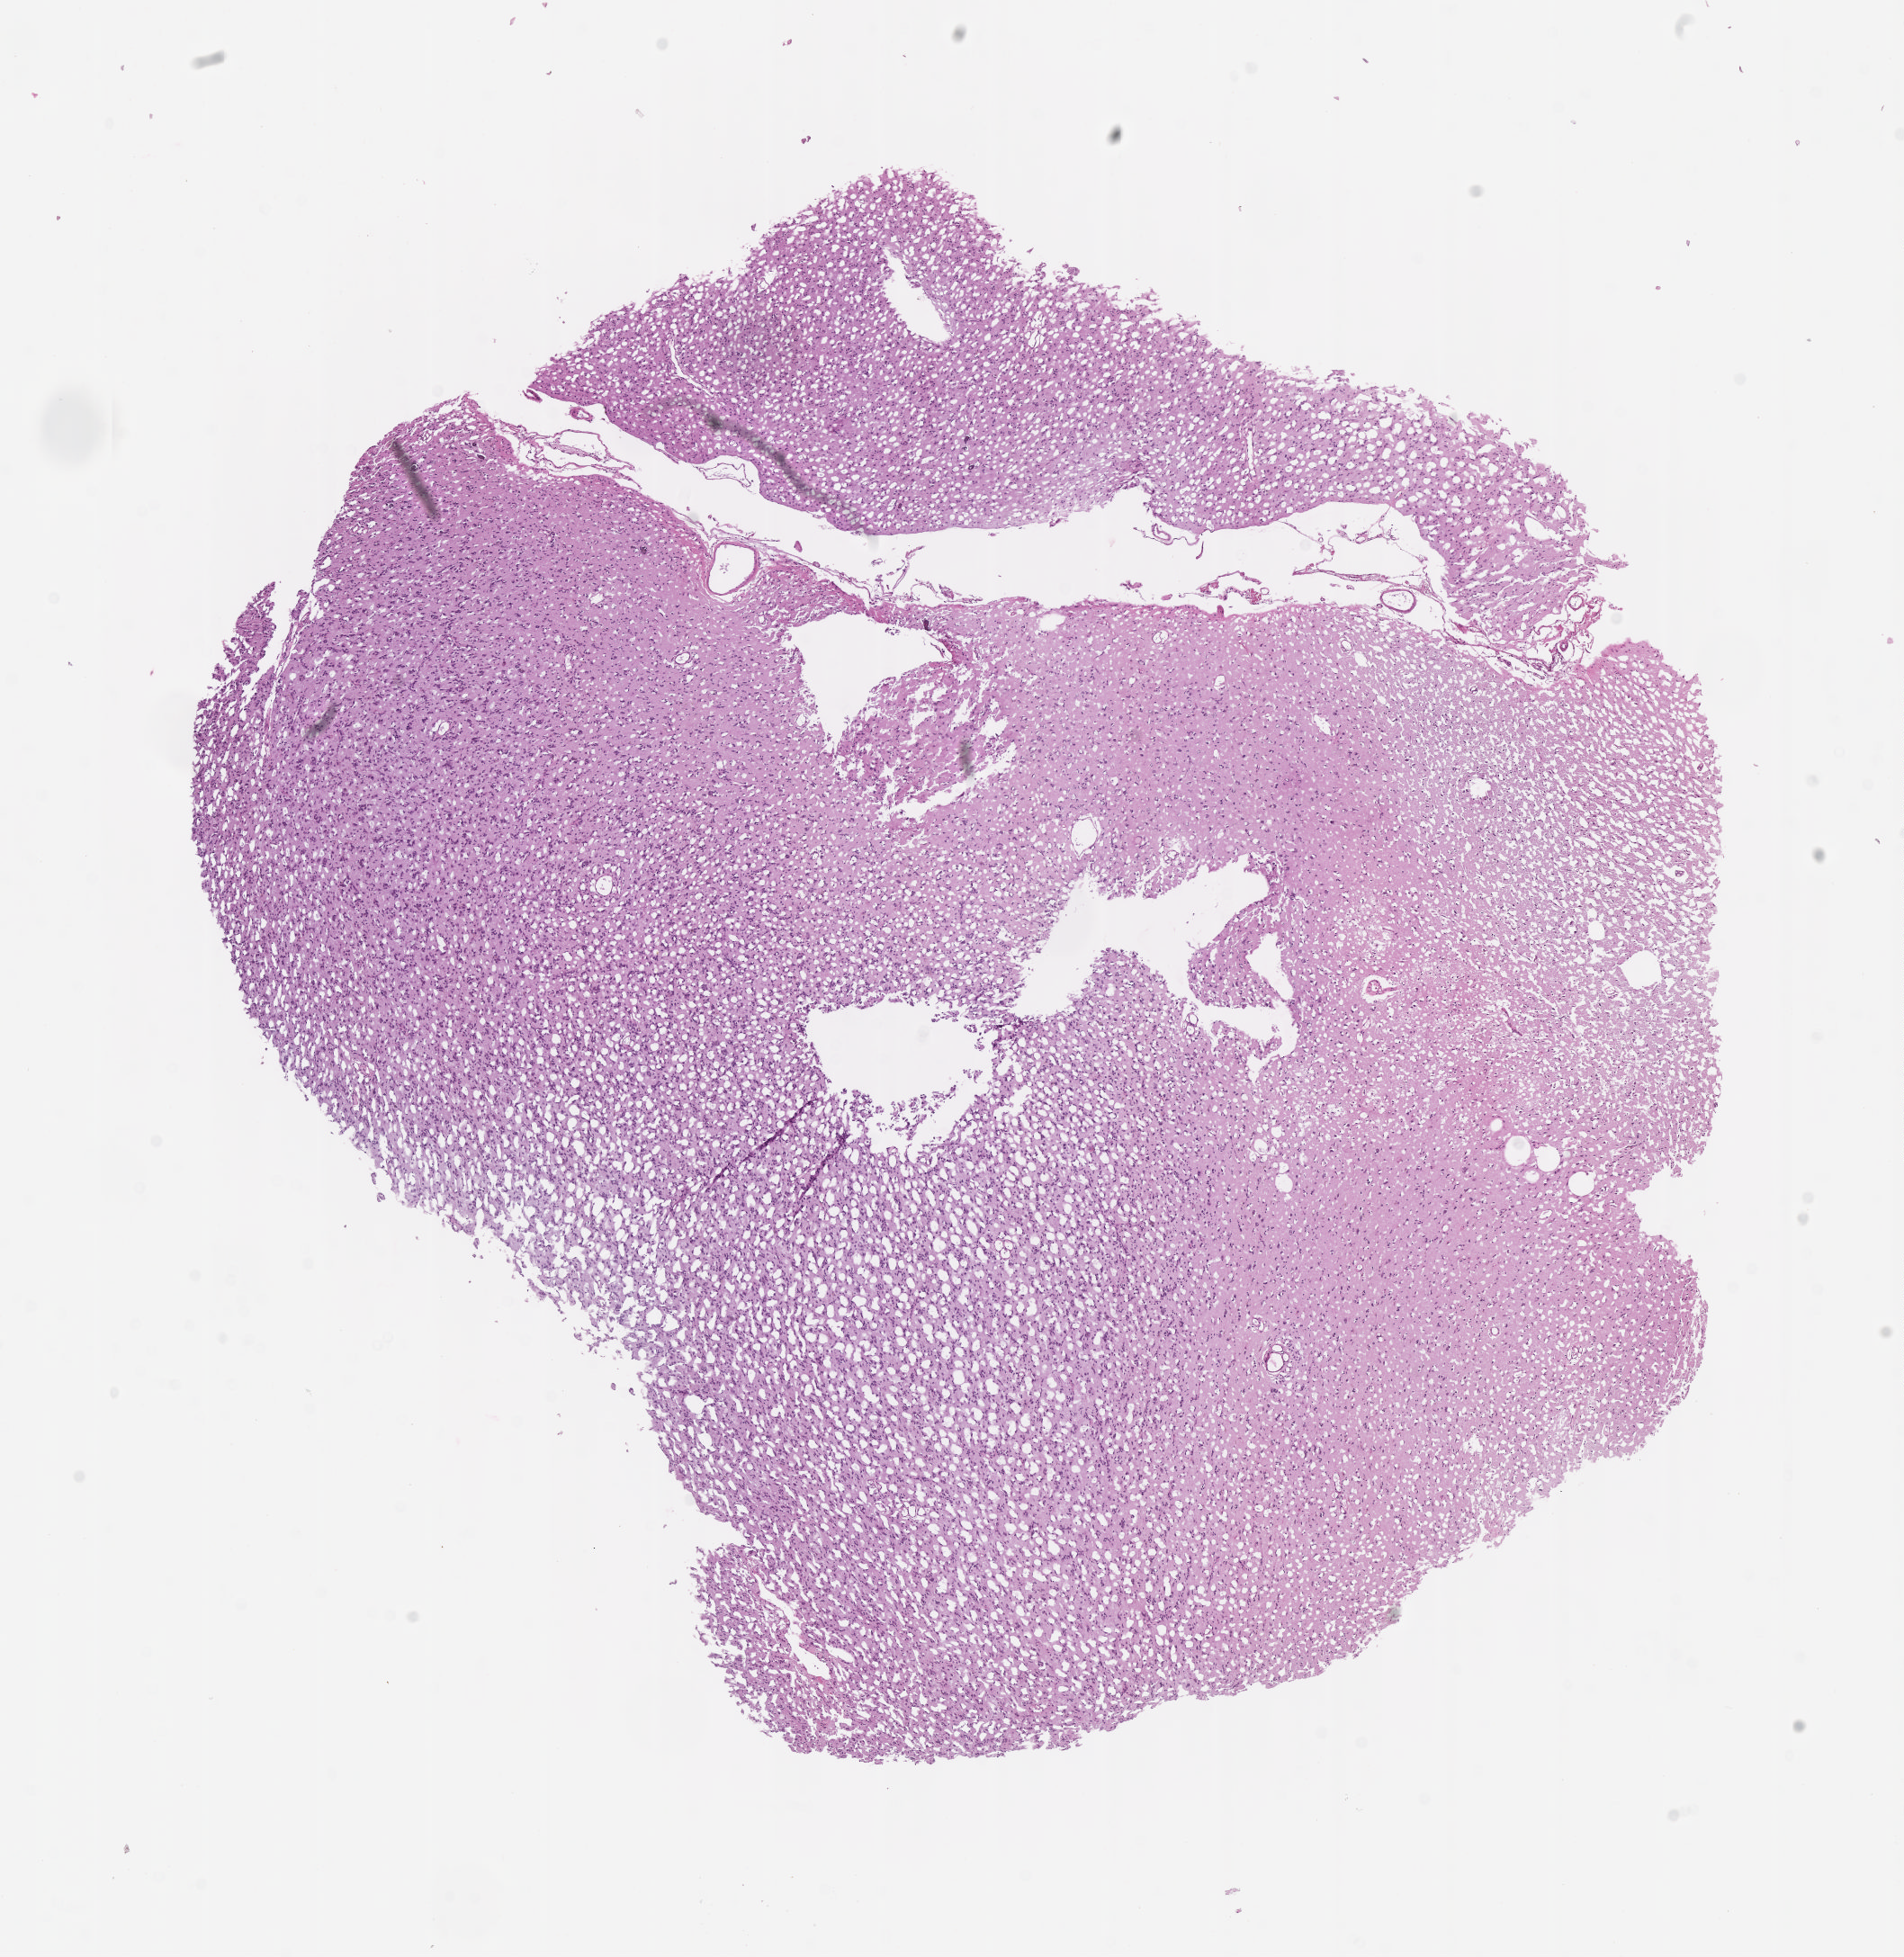
Whole-slide histology image, H&E — shown as a low-resolution overview of the whole scanned area (about 8.6 x 8.8 mm, acquisition: 40x scan). Formalin-fixed paraffin-embedded (FFPE) diagnostic section. Sample: primary tumour, brain. Male patient; age at initial diagnosis 86 years. Histologic grade: G2 (moderately differentiated).
• pathologic diagnosis: Oligodendroglioma, NOS (cerebrum)